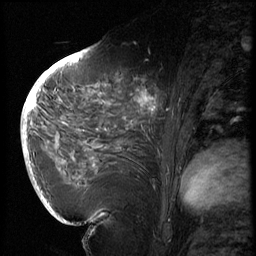
Breast MRI (dynamic contrast-enhanced), one sagittal slice. Position 34 of 72 along the scan axis. 3 images stored at this slice position (order not interpretable as contrast timing). 1.5 T. TE 4.2 ms, TR 8.9 ms. 256 × 256 image matrix. Patient: female, 56 years. Case-level facts recorded for this patient, not image findings: setting: breast cancer imaged before/during neoadjuvant chemotherapy.
Outlined on this slice (semi-automatically segmented with operator editing):
- analysis volume of interest (the breast-tissue region the enhancement analysis was run in; not a lesion): bounding box [x1, y1, x2, y2] px = [114, 76, 177, 138]
- tumour enhancement mask (voxels above the 140 % enhancement threshold inside the analysis volume of interest): [136, 90, 157, 118]